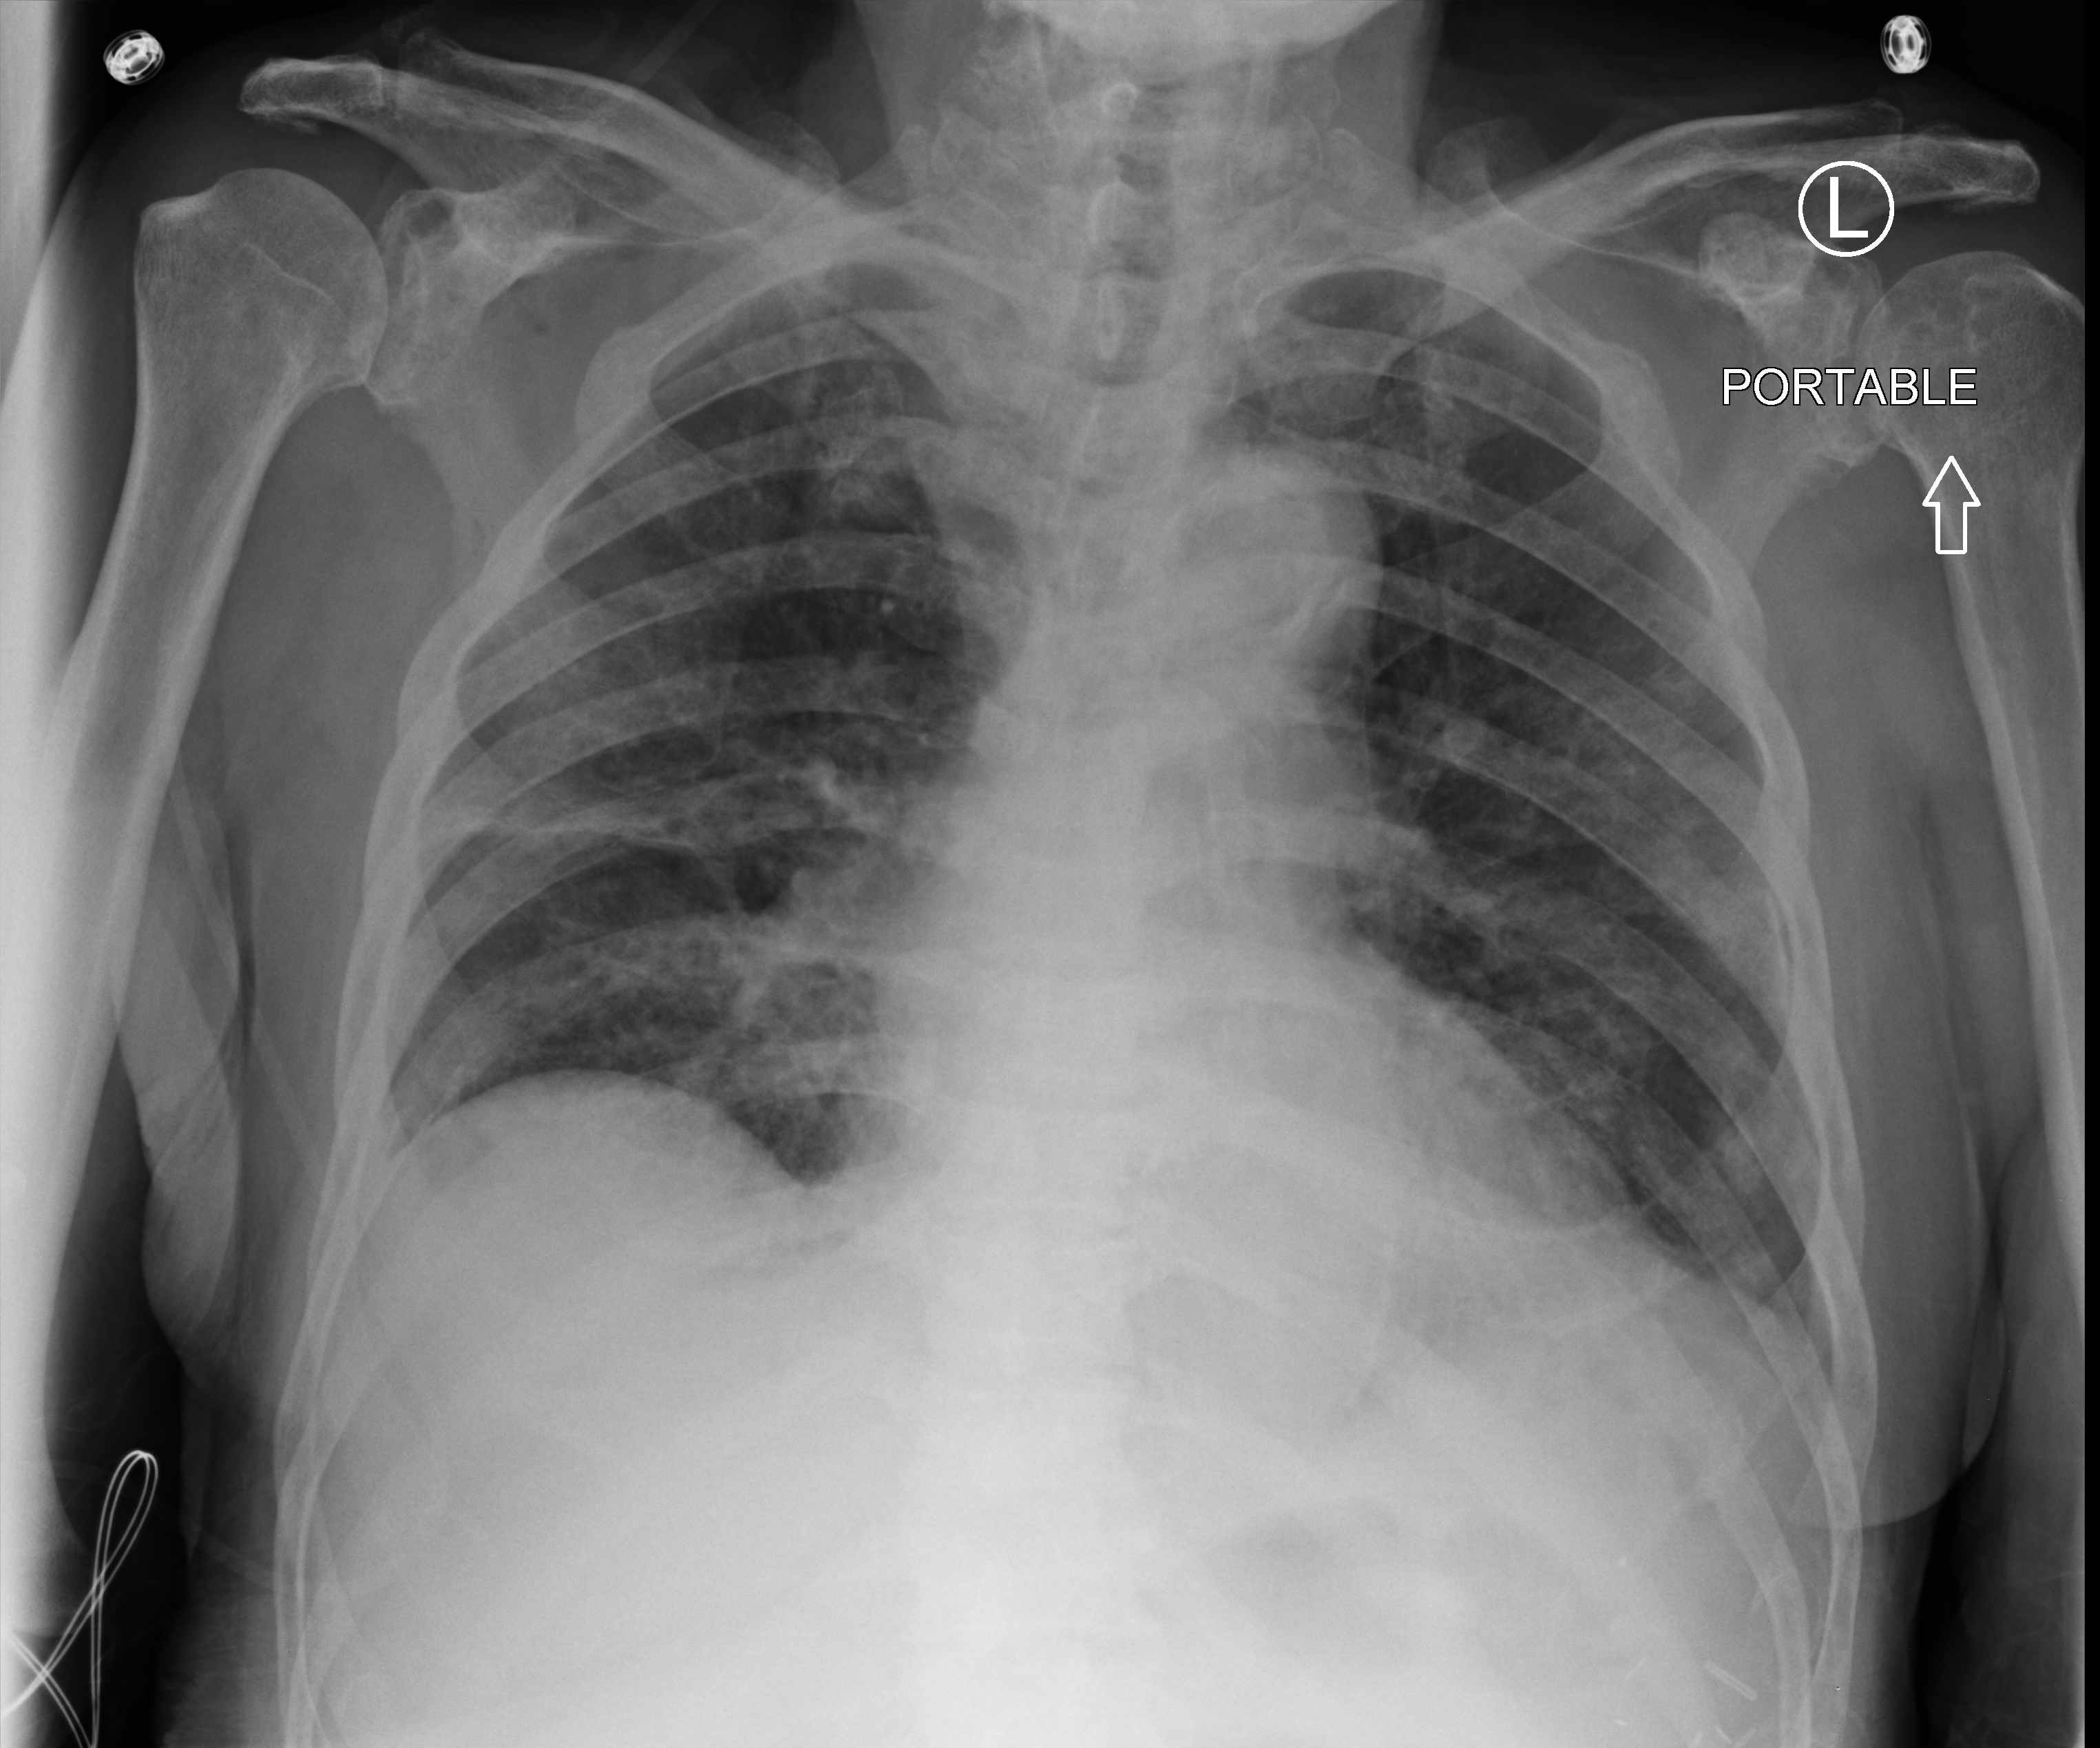
Portable chest radiograph; anteroposterior (AP) projection. Patient hospitalised with COVID-19; male, aged 75–90 years.
Admission-level facts for this patient (not findings on this image; timing relative to this image not recorded):
- length of hospital stay: 12 days
- admitted to intensive care during this hospital stay: no